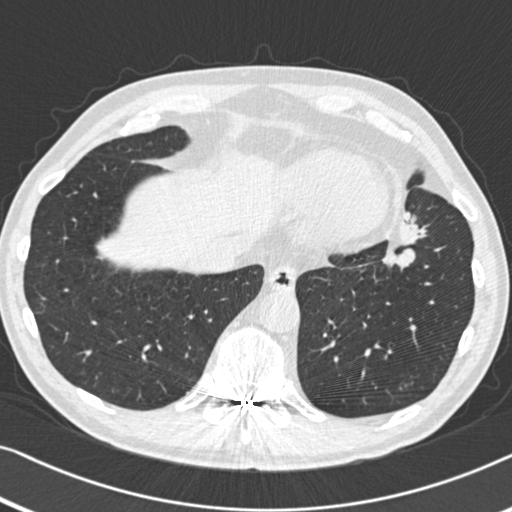
Low-dose screening chest CT, one axial slice; slice 122 of 383 in the series (ordered by position); reconstruction kernel B30f; lung window (W 1500 / L -600 HU); 1 mm slice thickness; 512 × 512 image matrix, field of view 332 × 332 mm.
Structures marked on this image (expert manual segmentation):
- lesion 1 (tumor, upper lobe of left lung): bounding box [x1, y1, x2, y2] px = [384, 213, 426, 268]